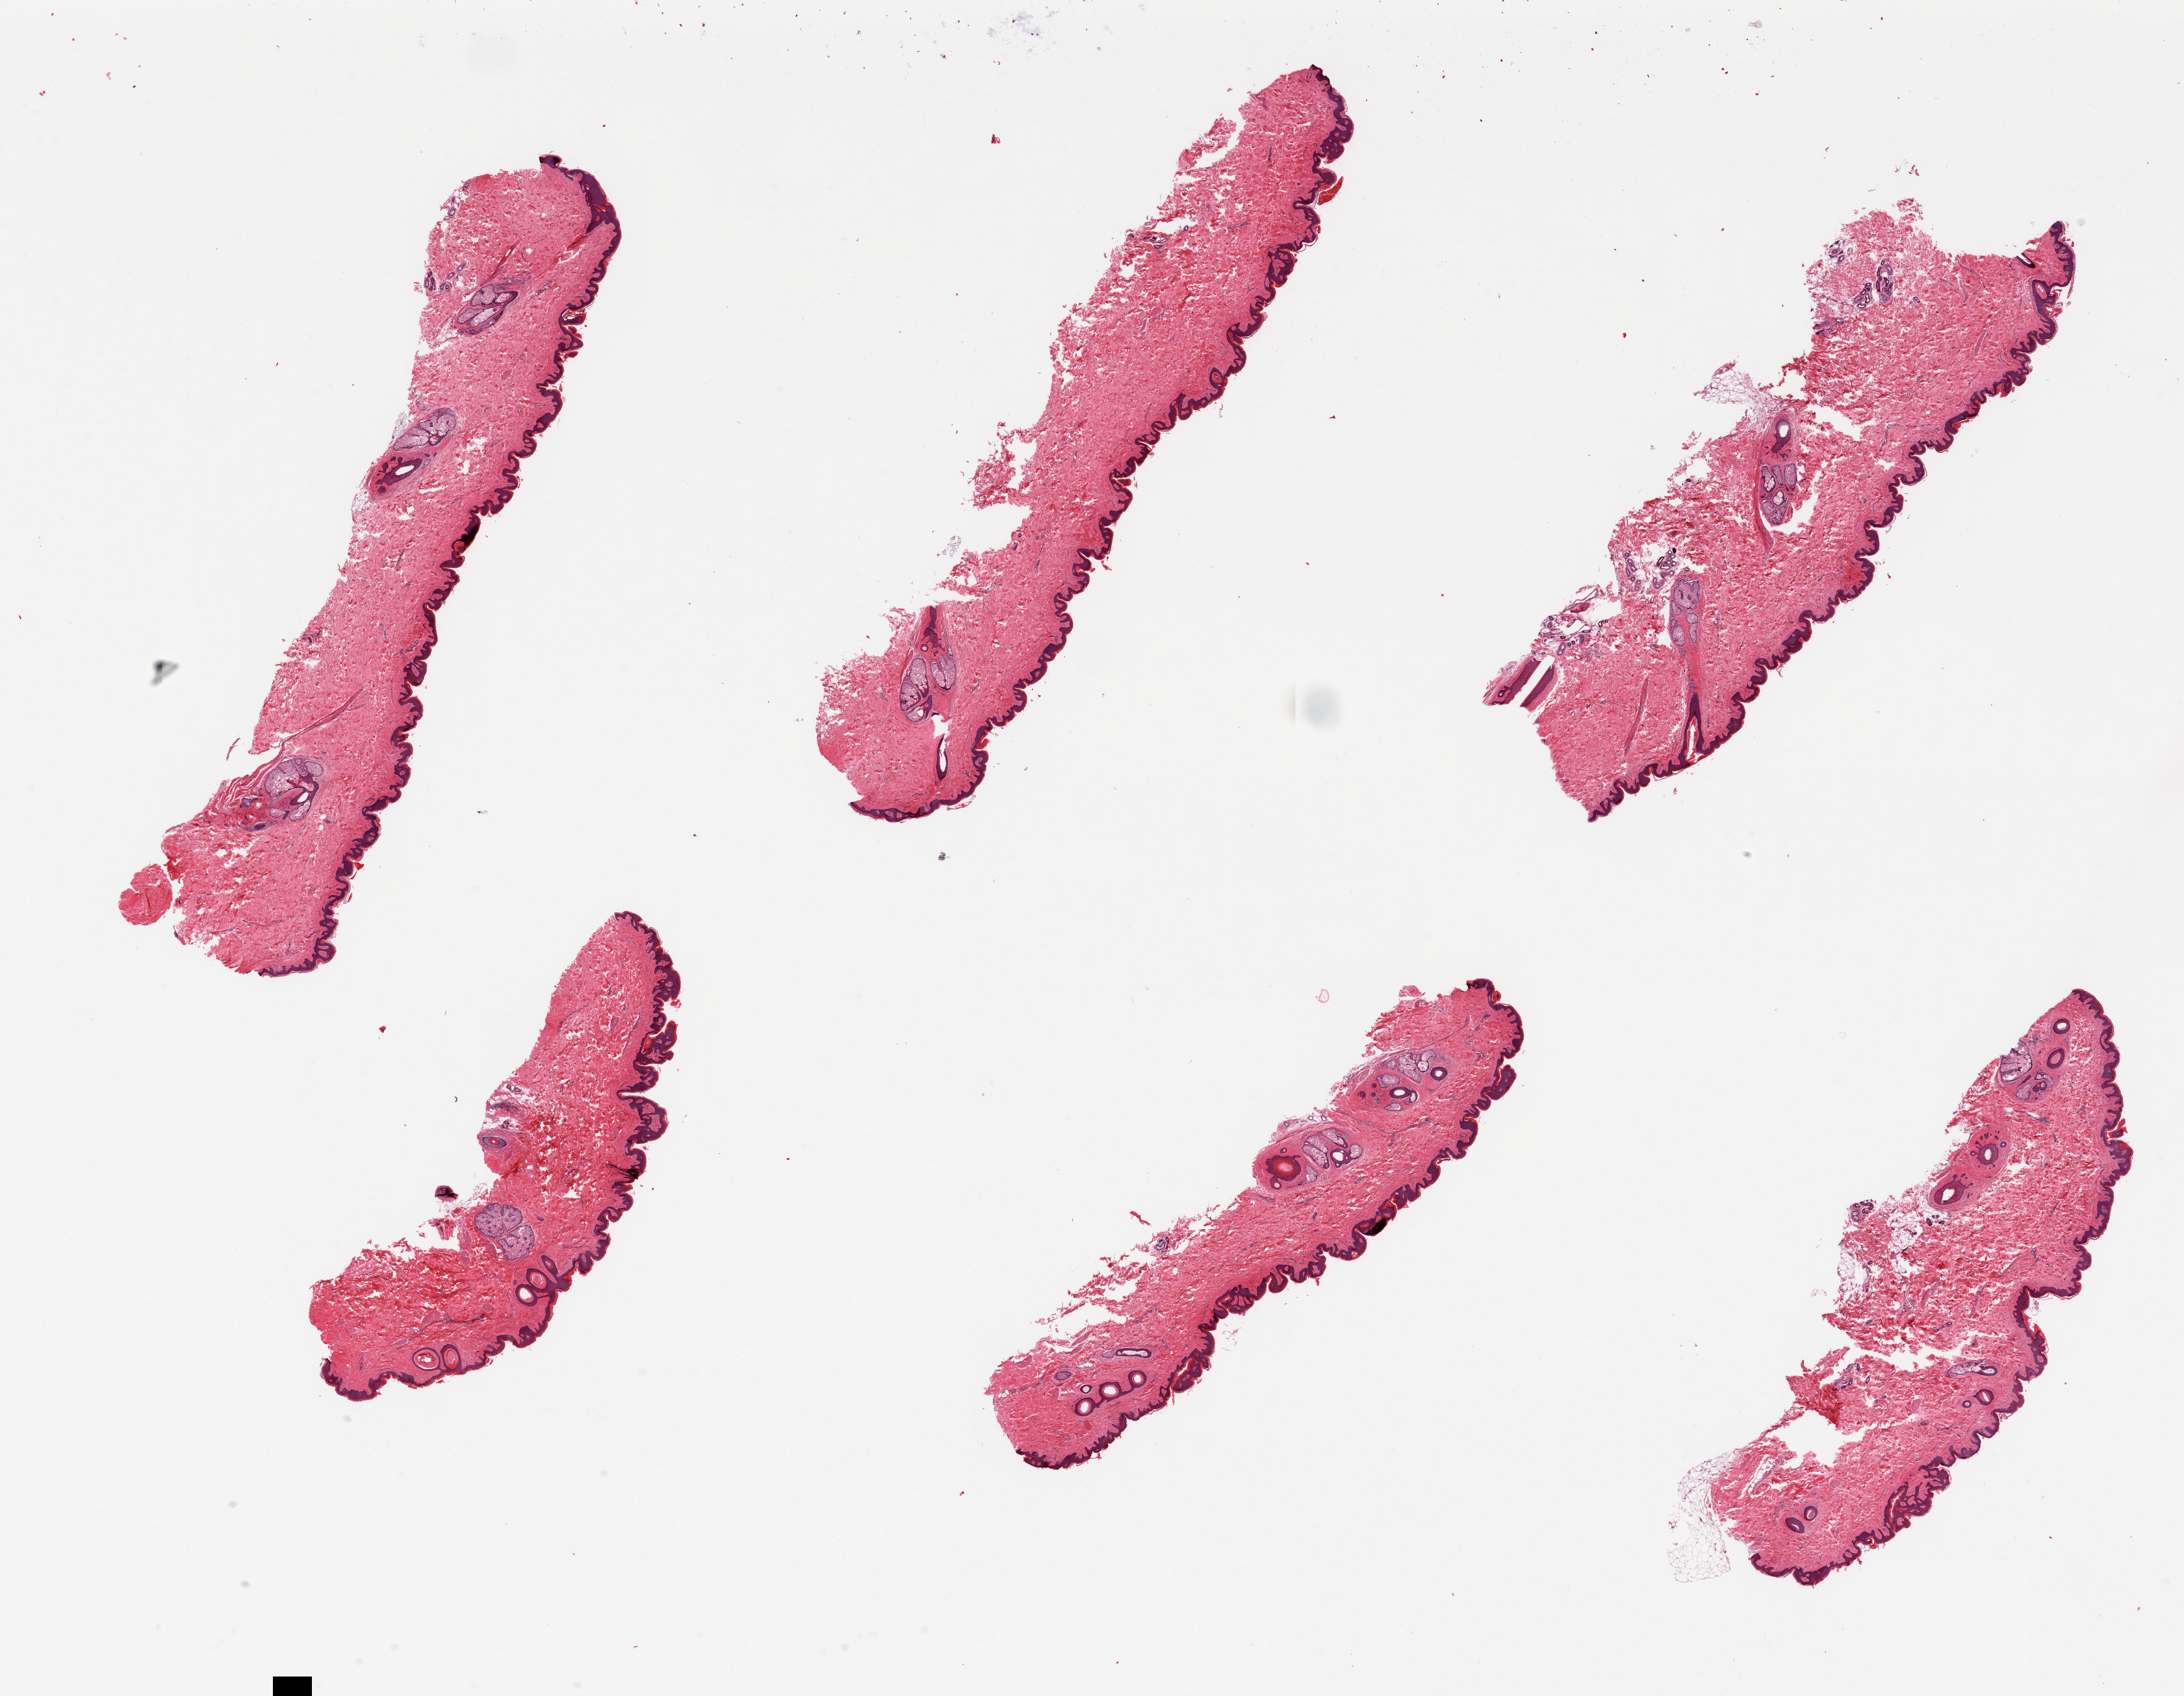
Hematoxylin and eosin (H&E) whole-slide image, brightfield — whole scanned area (about 26.6 x 20.6 mm) shown as a low-resolution overview. PAXgene-fixed, paraffin-embedded tissue. Sampled site (target tissue): skin of suprapubic region. Donor tissue sample. Male donor.
* review note (as recorded): 6 pieces; ~ 5% internal (periadnexal) fat